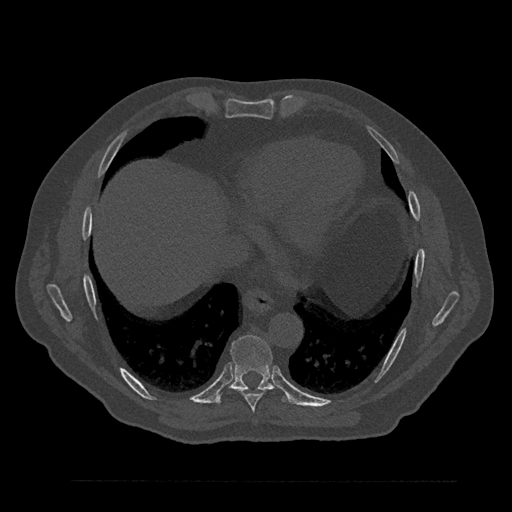
CT including the spine, one axial slice; position 429 of 797 along the scan axis; bone window (W 1800 / L 400 HU); 512 × 512 image matrix. Male patient, age 61 years. Case-level facts recorded for this patient, not image findings: primary cancer: prostate.
Outlined on this slice (semi-automatically segmented with operator editing):
- T8 vertebra: bounding box (x1, y1, x2, y2) in pixels: (237, 388, 271, 412)
- T9 vertebra: (214, 335, 291, 406)